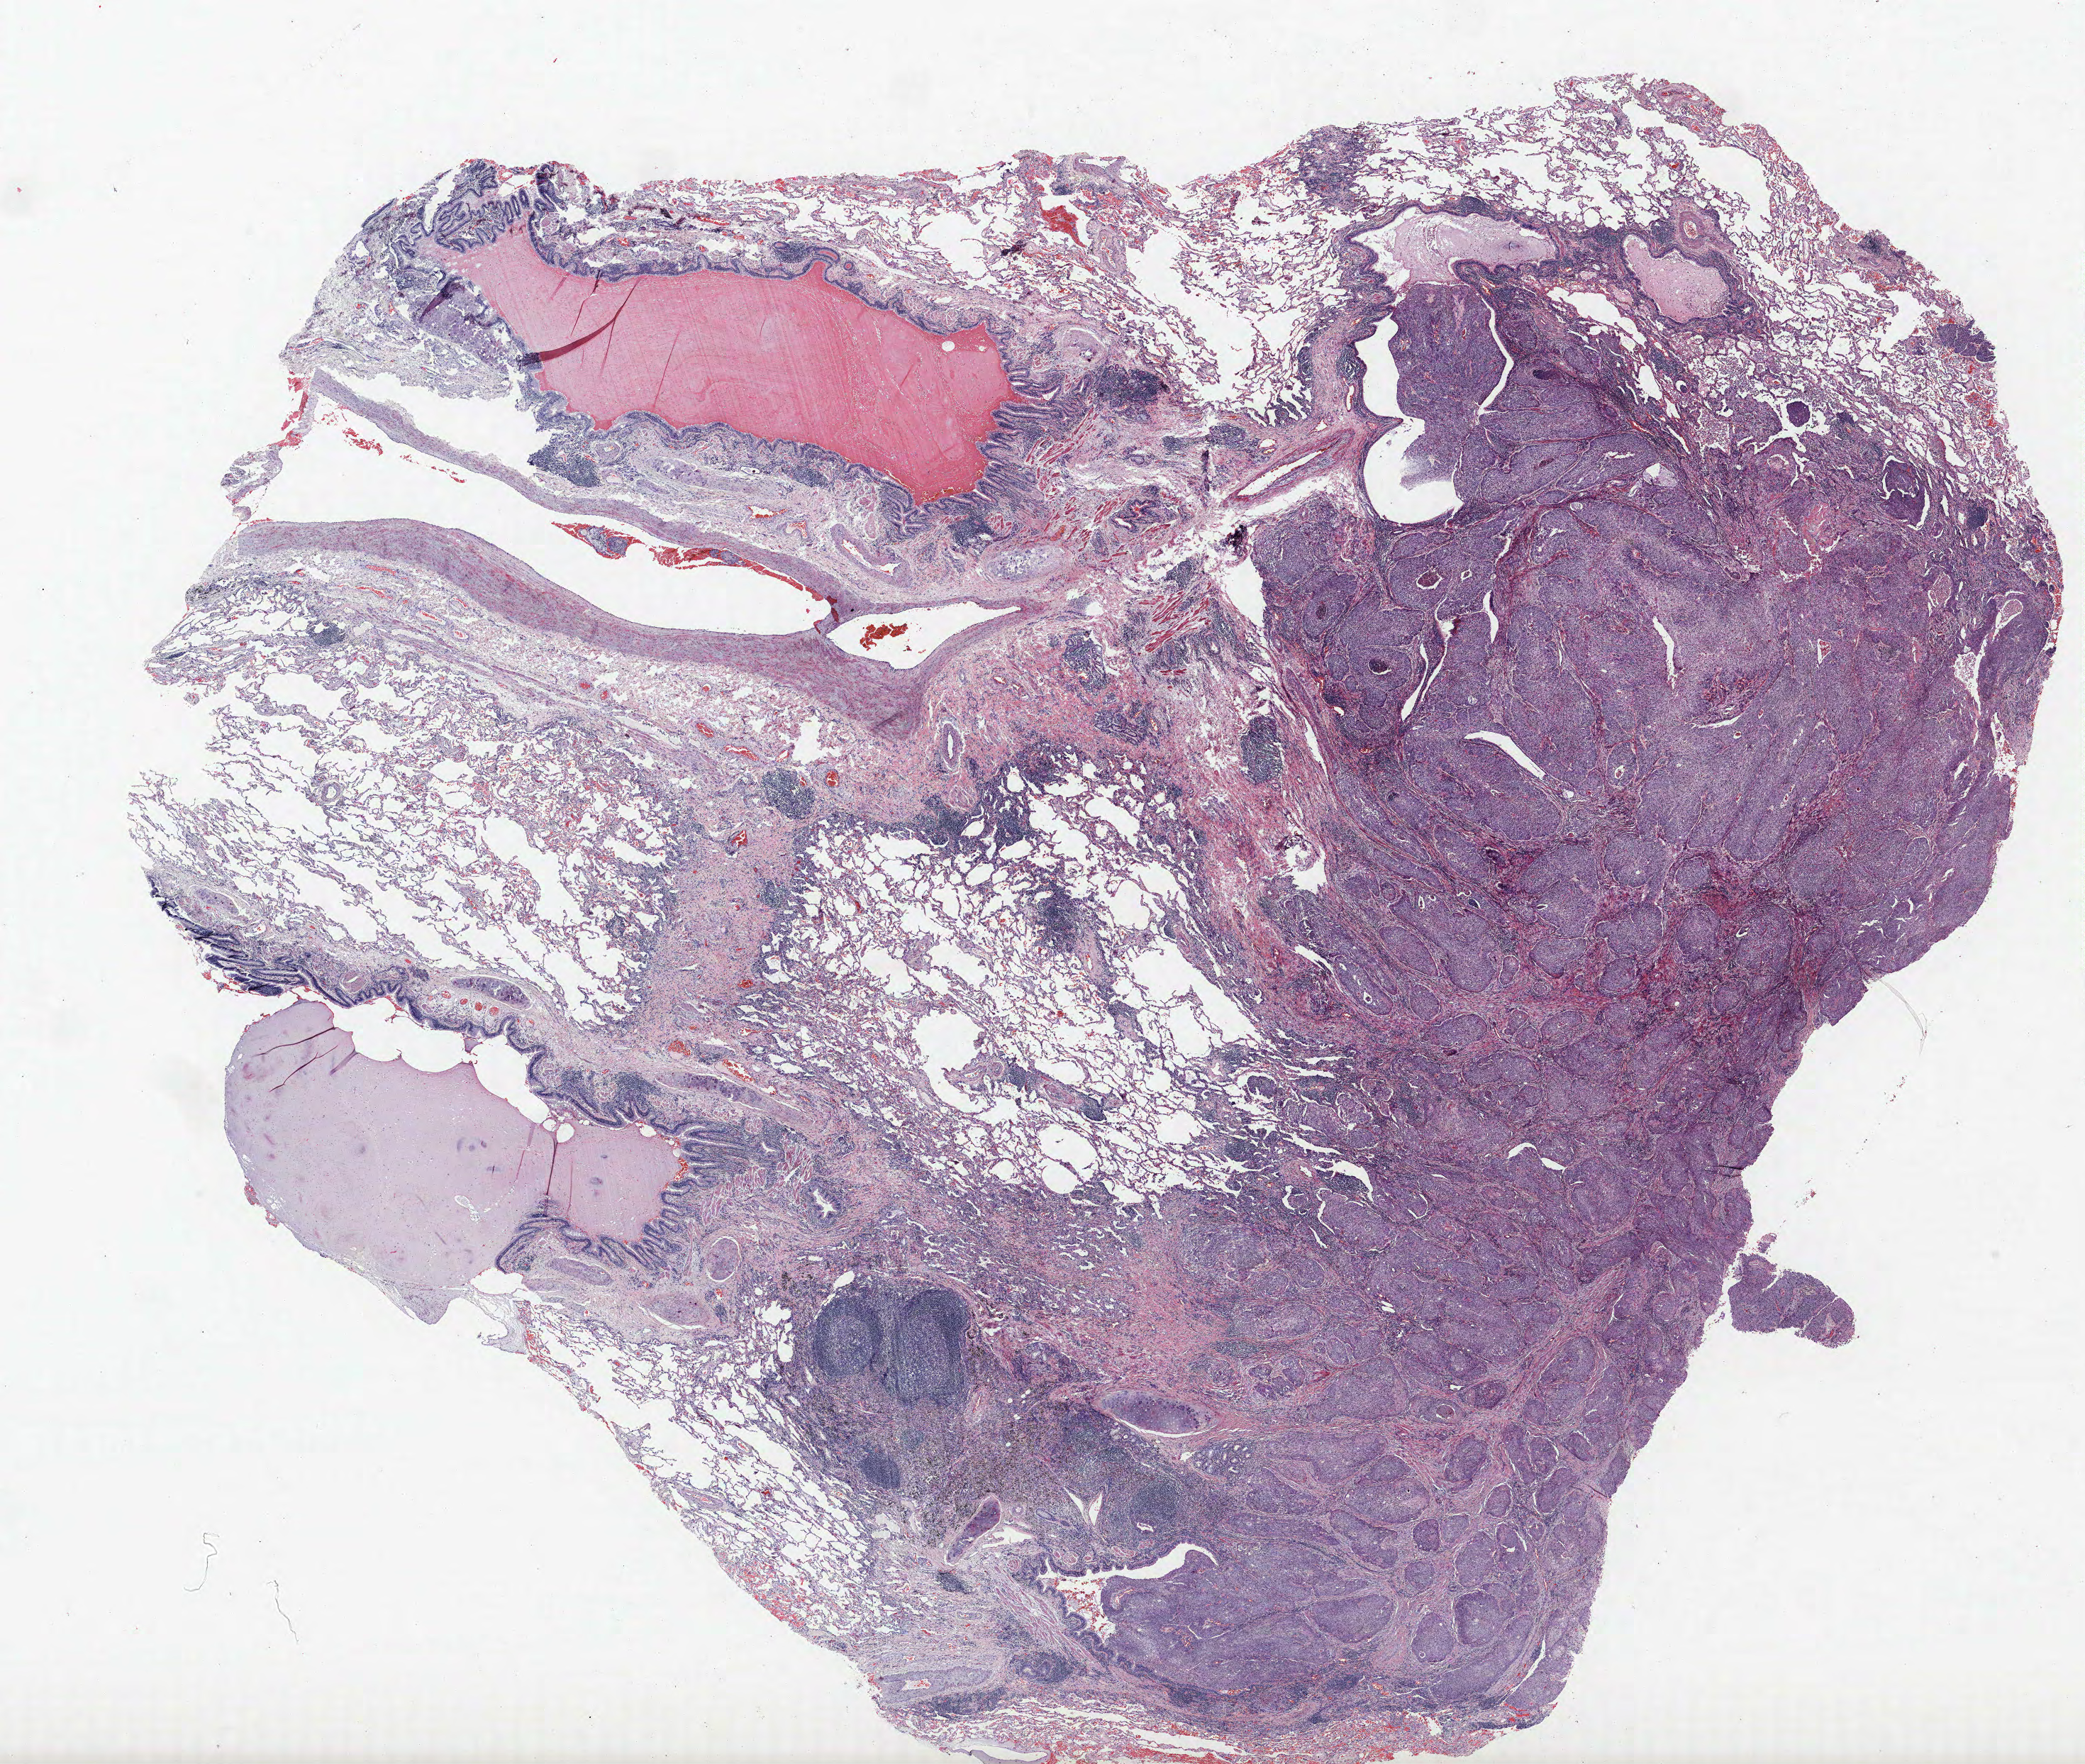
Whole-slide histology image, H&E, low-resolution overview of the scanned area, about 23.5 x 19.9 mm (from a 40x scan), formalin-fixed paraffin-embedded (FFPE) section, lung tissue. Male, age 72 at enrolment. Grade: poorly differentiated (G3).
Participant's lung-cancer diagnosis: Squamous cell carcinoma, NOS (ICD-O-3 8070/3). ICD-O-3 topography: upper lobe of lung (C34.1). Tumour size (pathology): 30 mm. Stage (AJCC 6th edition): IA. Primary tumour location (clinical record): right upper lobe.